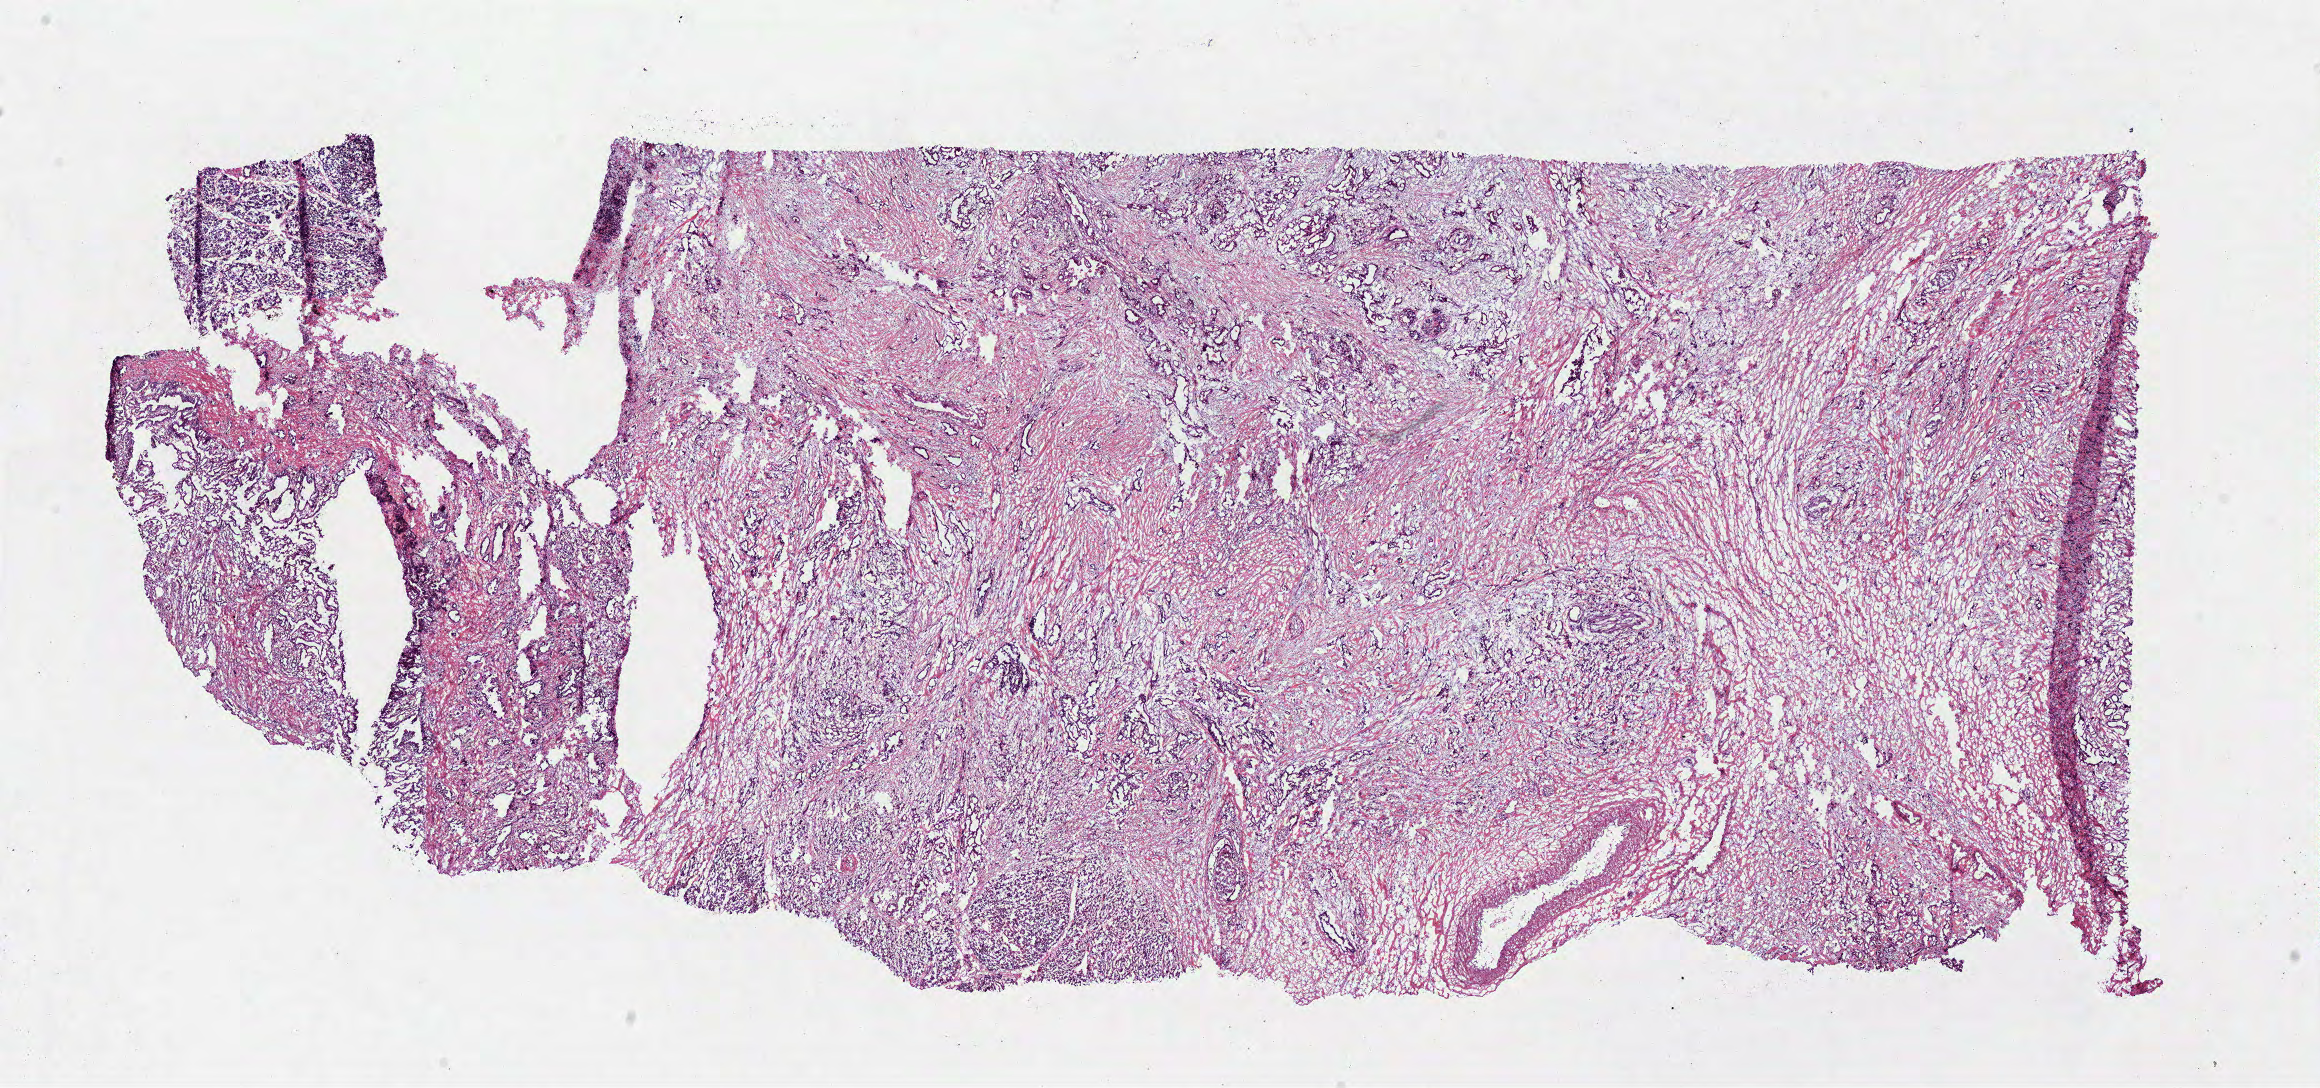
Digitized H&E-stained tissue section (whole slide) — a low-resolution overview of the entire scanned area, about 18.3 x 8.6 mm, frozen section, pancreas, primary tumour sample. Male patient; age at initial diagnosis 52 years. Histologic grade: G3 (poorly differentiated). Slide review estimates, as recorded: tumour cells 55%, tumour nuclei 75%, normal cells 5%, stromal cells 40%, necrosis 0%.
AJCC pathologic stage: IIB (6th edition). Histologic diagnosis: Infiltrating duct carcinoma, NOS (head of pancreas). Lymph nodes positive (case pathology): 3 of 9 examined.